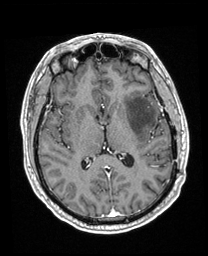
Brain MRI from a brain-tumour surgery series, one axial slice. Position 104 of 208 along the scan axis. T1-weighted post-contrast. 1 mm slice thickness. 208 × 256 image matrix. From the clinical record (not read from this slice): histopathology: Astrocytoma; WHO grade: 3; IDH mutation: yes.
Outlined on this slice (manually delineated by an expert):
- previous resection cavity: bounding box <155,124,162,135> (left, top, right, bottom; pixels)